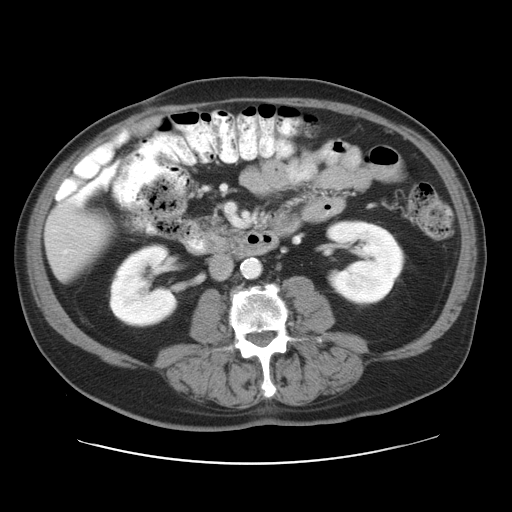
Contrast-enhanced abdominal CT, one axial slice; slice 9 of 28 in the series (ordered by position); intravenous contrast given; soft-tissue window (W 400 / L 40 HU); 512 × 512 image matrix. Male patient, age 74 years. From the clinical record (not read from this slice): diagnosis: colorectal cancer liver metastases, imaged before liver resection; multiple liver metastases: no; largest metastasis: 5 cm; disease in both lobes: no.
Structures marked on this image (manually delineated by an expert):
- liver: box from (x=47, y=211) to (x=105, y=277) px
- planned liver remnant (the part of the liver to remain after resection): (x=47, y=210)–(x=105, y=277)